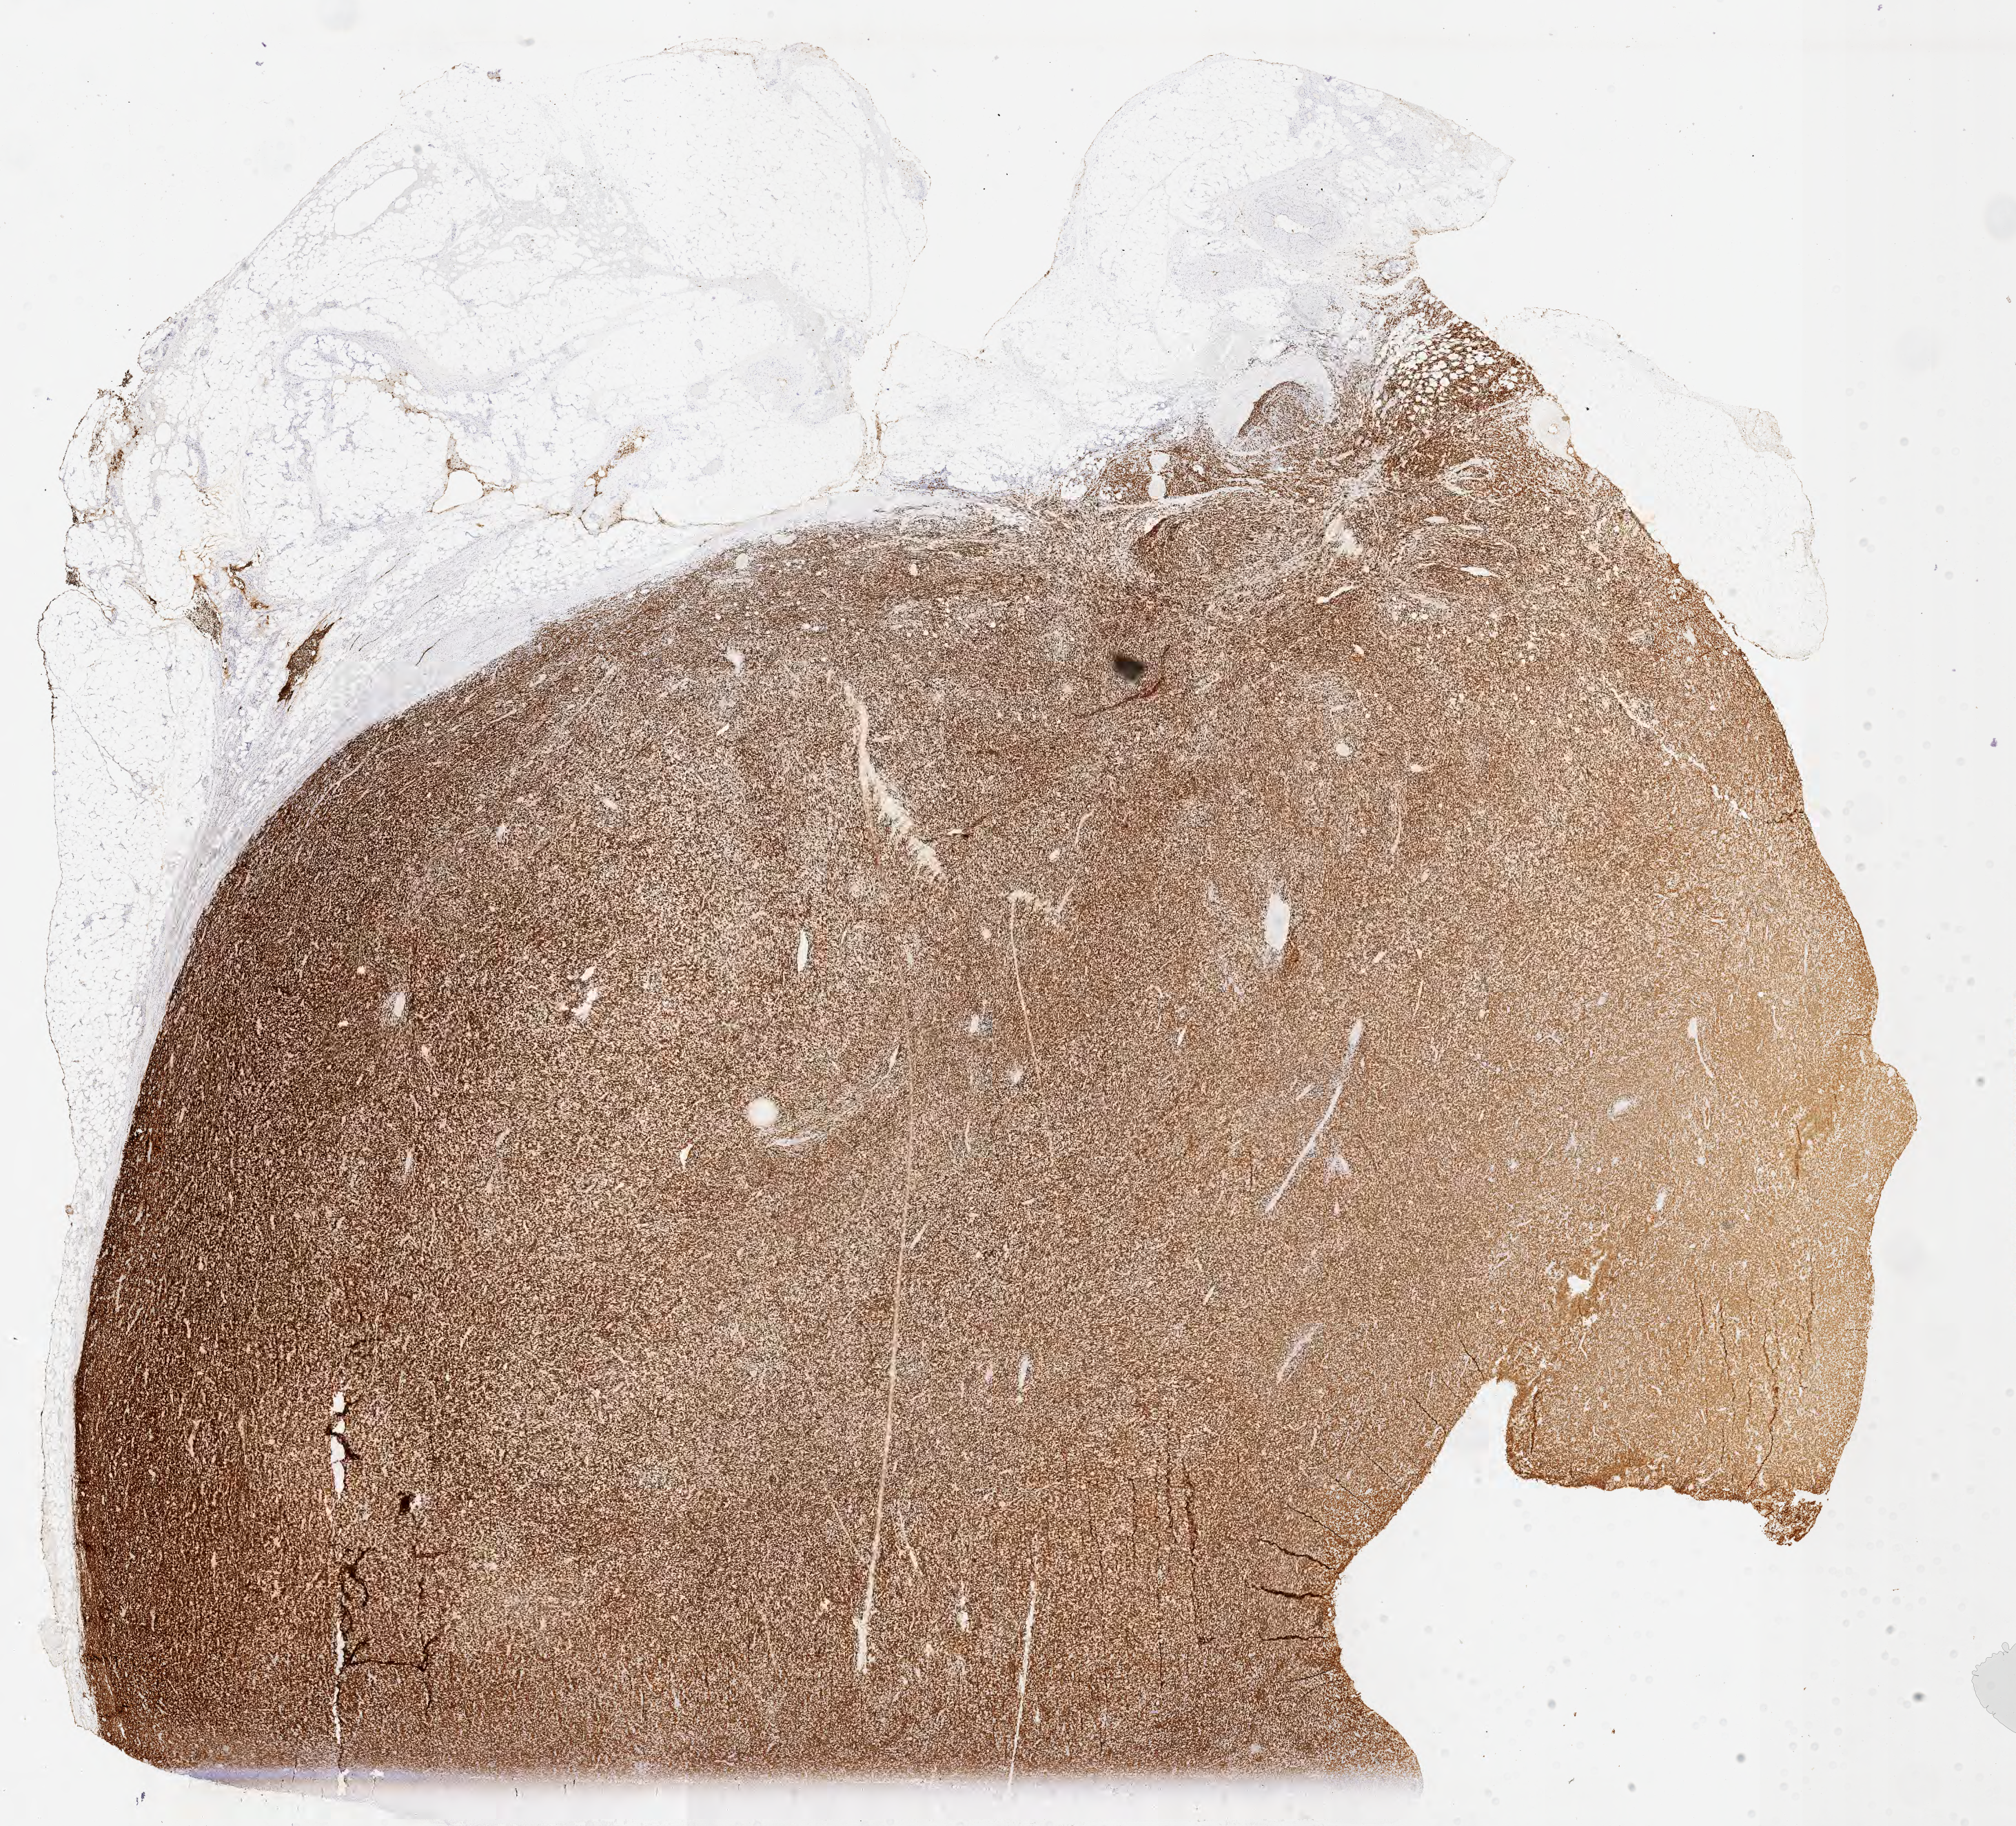
Whole-slide image, immunohistochemical stain for CD79a, whole scanned area (about 23.6 x 21.4 mm) shown as a low-resolution overview; tumor tissue; anatomic site: lymph node. Patient male; 54 years old.
Diagnosis: Diffuse large B-cell lymphoma, NOS.